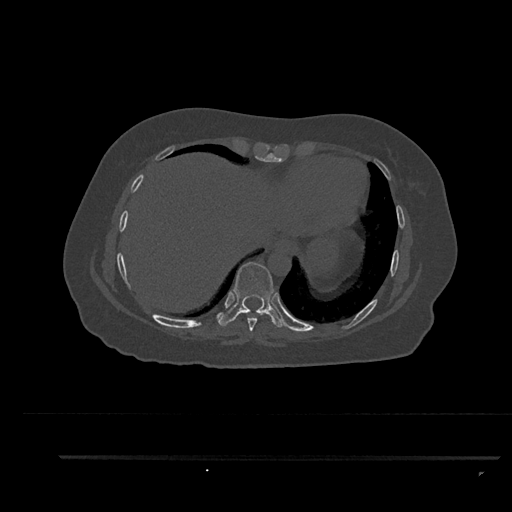
CT including the spine, one axial slice. Position 430 of 797 along the scan axis. Reconstruction kernel Br40s/3. Bone window (W 1800 / L 400 HU). 0.5 mm slice thickness. 512 × 512 image matrix. Patient: female, 44 years. Case-level facts recorded for this patient, not image findings: primary cancer: renal.
Annotated regions visible in this slice (semi-automatic segmentation, software-assisted and operator-edited):
- T8 vertebra: bounding box <245,310,263,331> (left, top, right, bottom; pixels)
- T9 vertebra: <217,262,286,328>